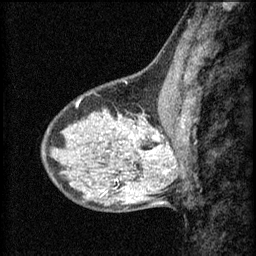
Breast MRI (dynamic contrast-enhanced), one sagittal slice. Slice 21 of 60 in the series (ordered by position). 3 images stored at this slice position (order not interpretable as contrast timing). 1.5 T. TE 4.2 ms, TR 8.2 ms. 256 × 256 image matrix, field of view 180 × 180 mm. Female patient, age 40 years.
Annotated regions visible in this slice (semi-automatic segmentation, software-assisted and operator-edited):
- analysis volume of interest (the breast-tissue region the enhancement analysis was run in; not a lesion): bounding box <108,108,167,159> (left, top, right, bottom; pixels)
- tumour enhancement mask (voxels above the 70 % enhancement threshold inside the analysis volume of interest): <120,116,167,153>